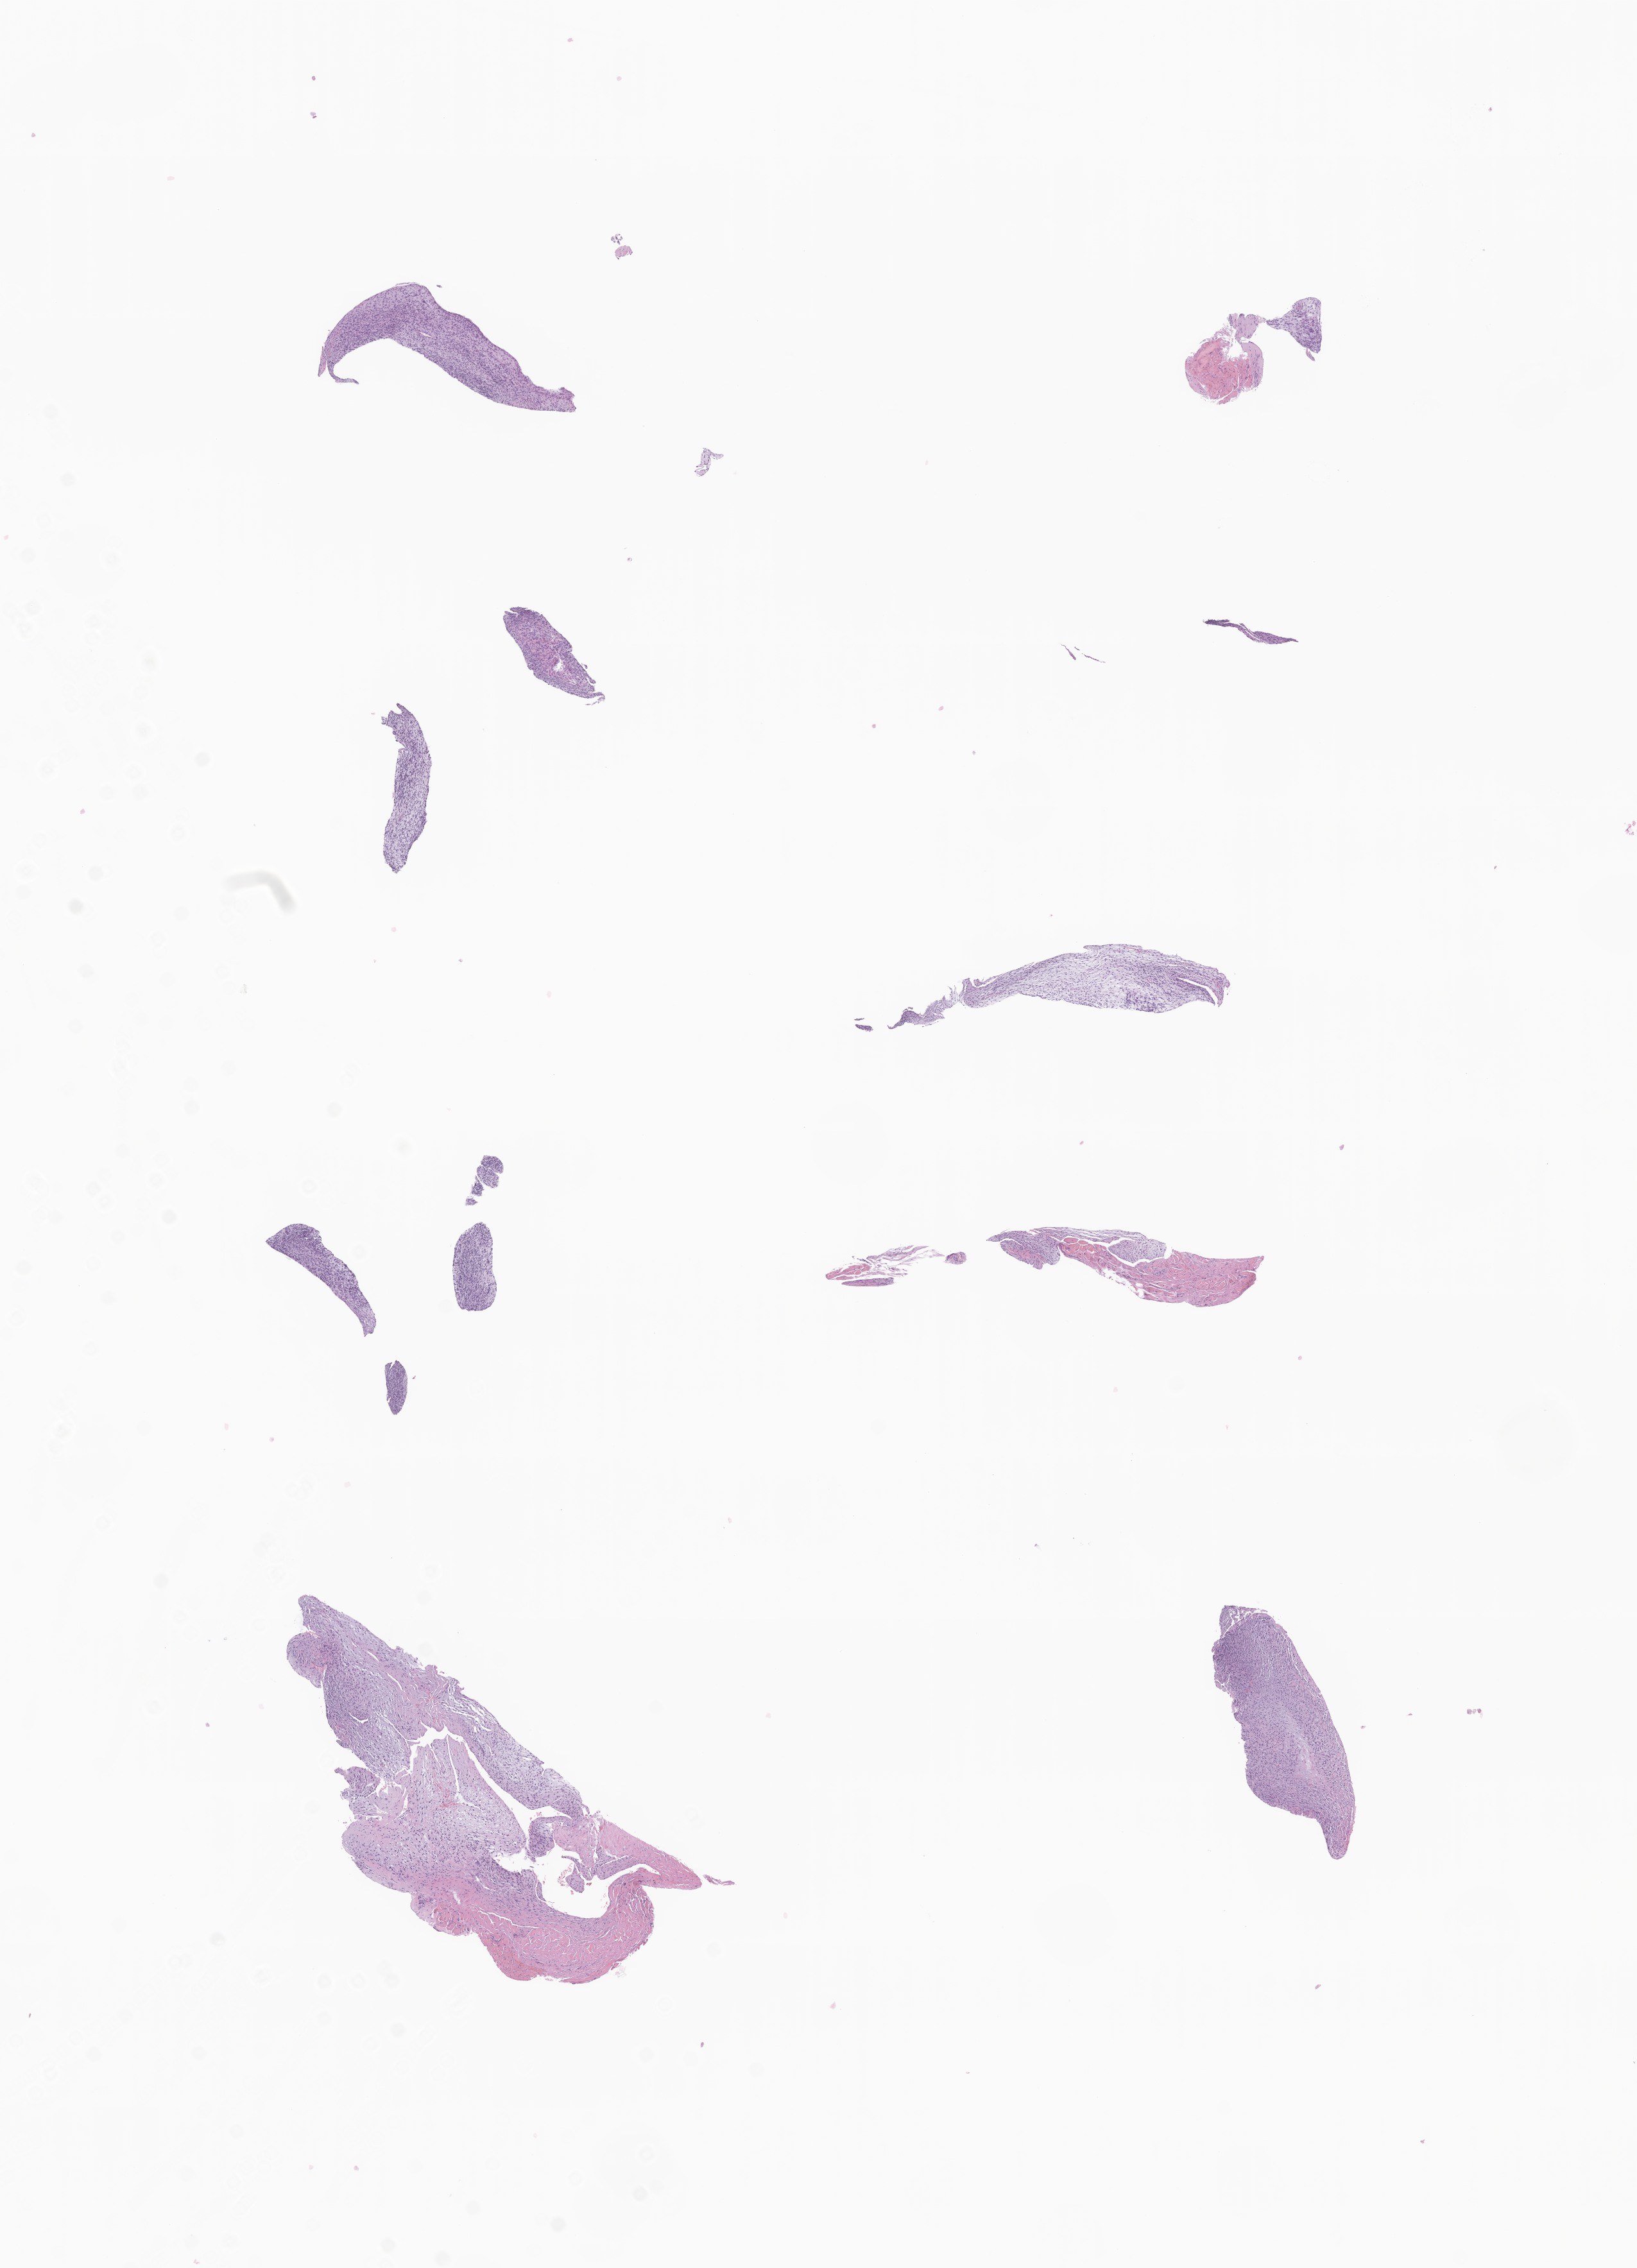
Whole-slide image, haematoxylin and eosin stain of tumor tissue from the pharynx — shown as a low-resolution overview of the whole scanned area (about 10.8 x 14.9 mm); formalin-fixed, paraffin-embedded (FFPE) tissue. Patient male; age 62 months (5 years 2 months).
• recorded diagnosis: Embryonal rhabdomyosarcoma, NOS